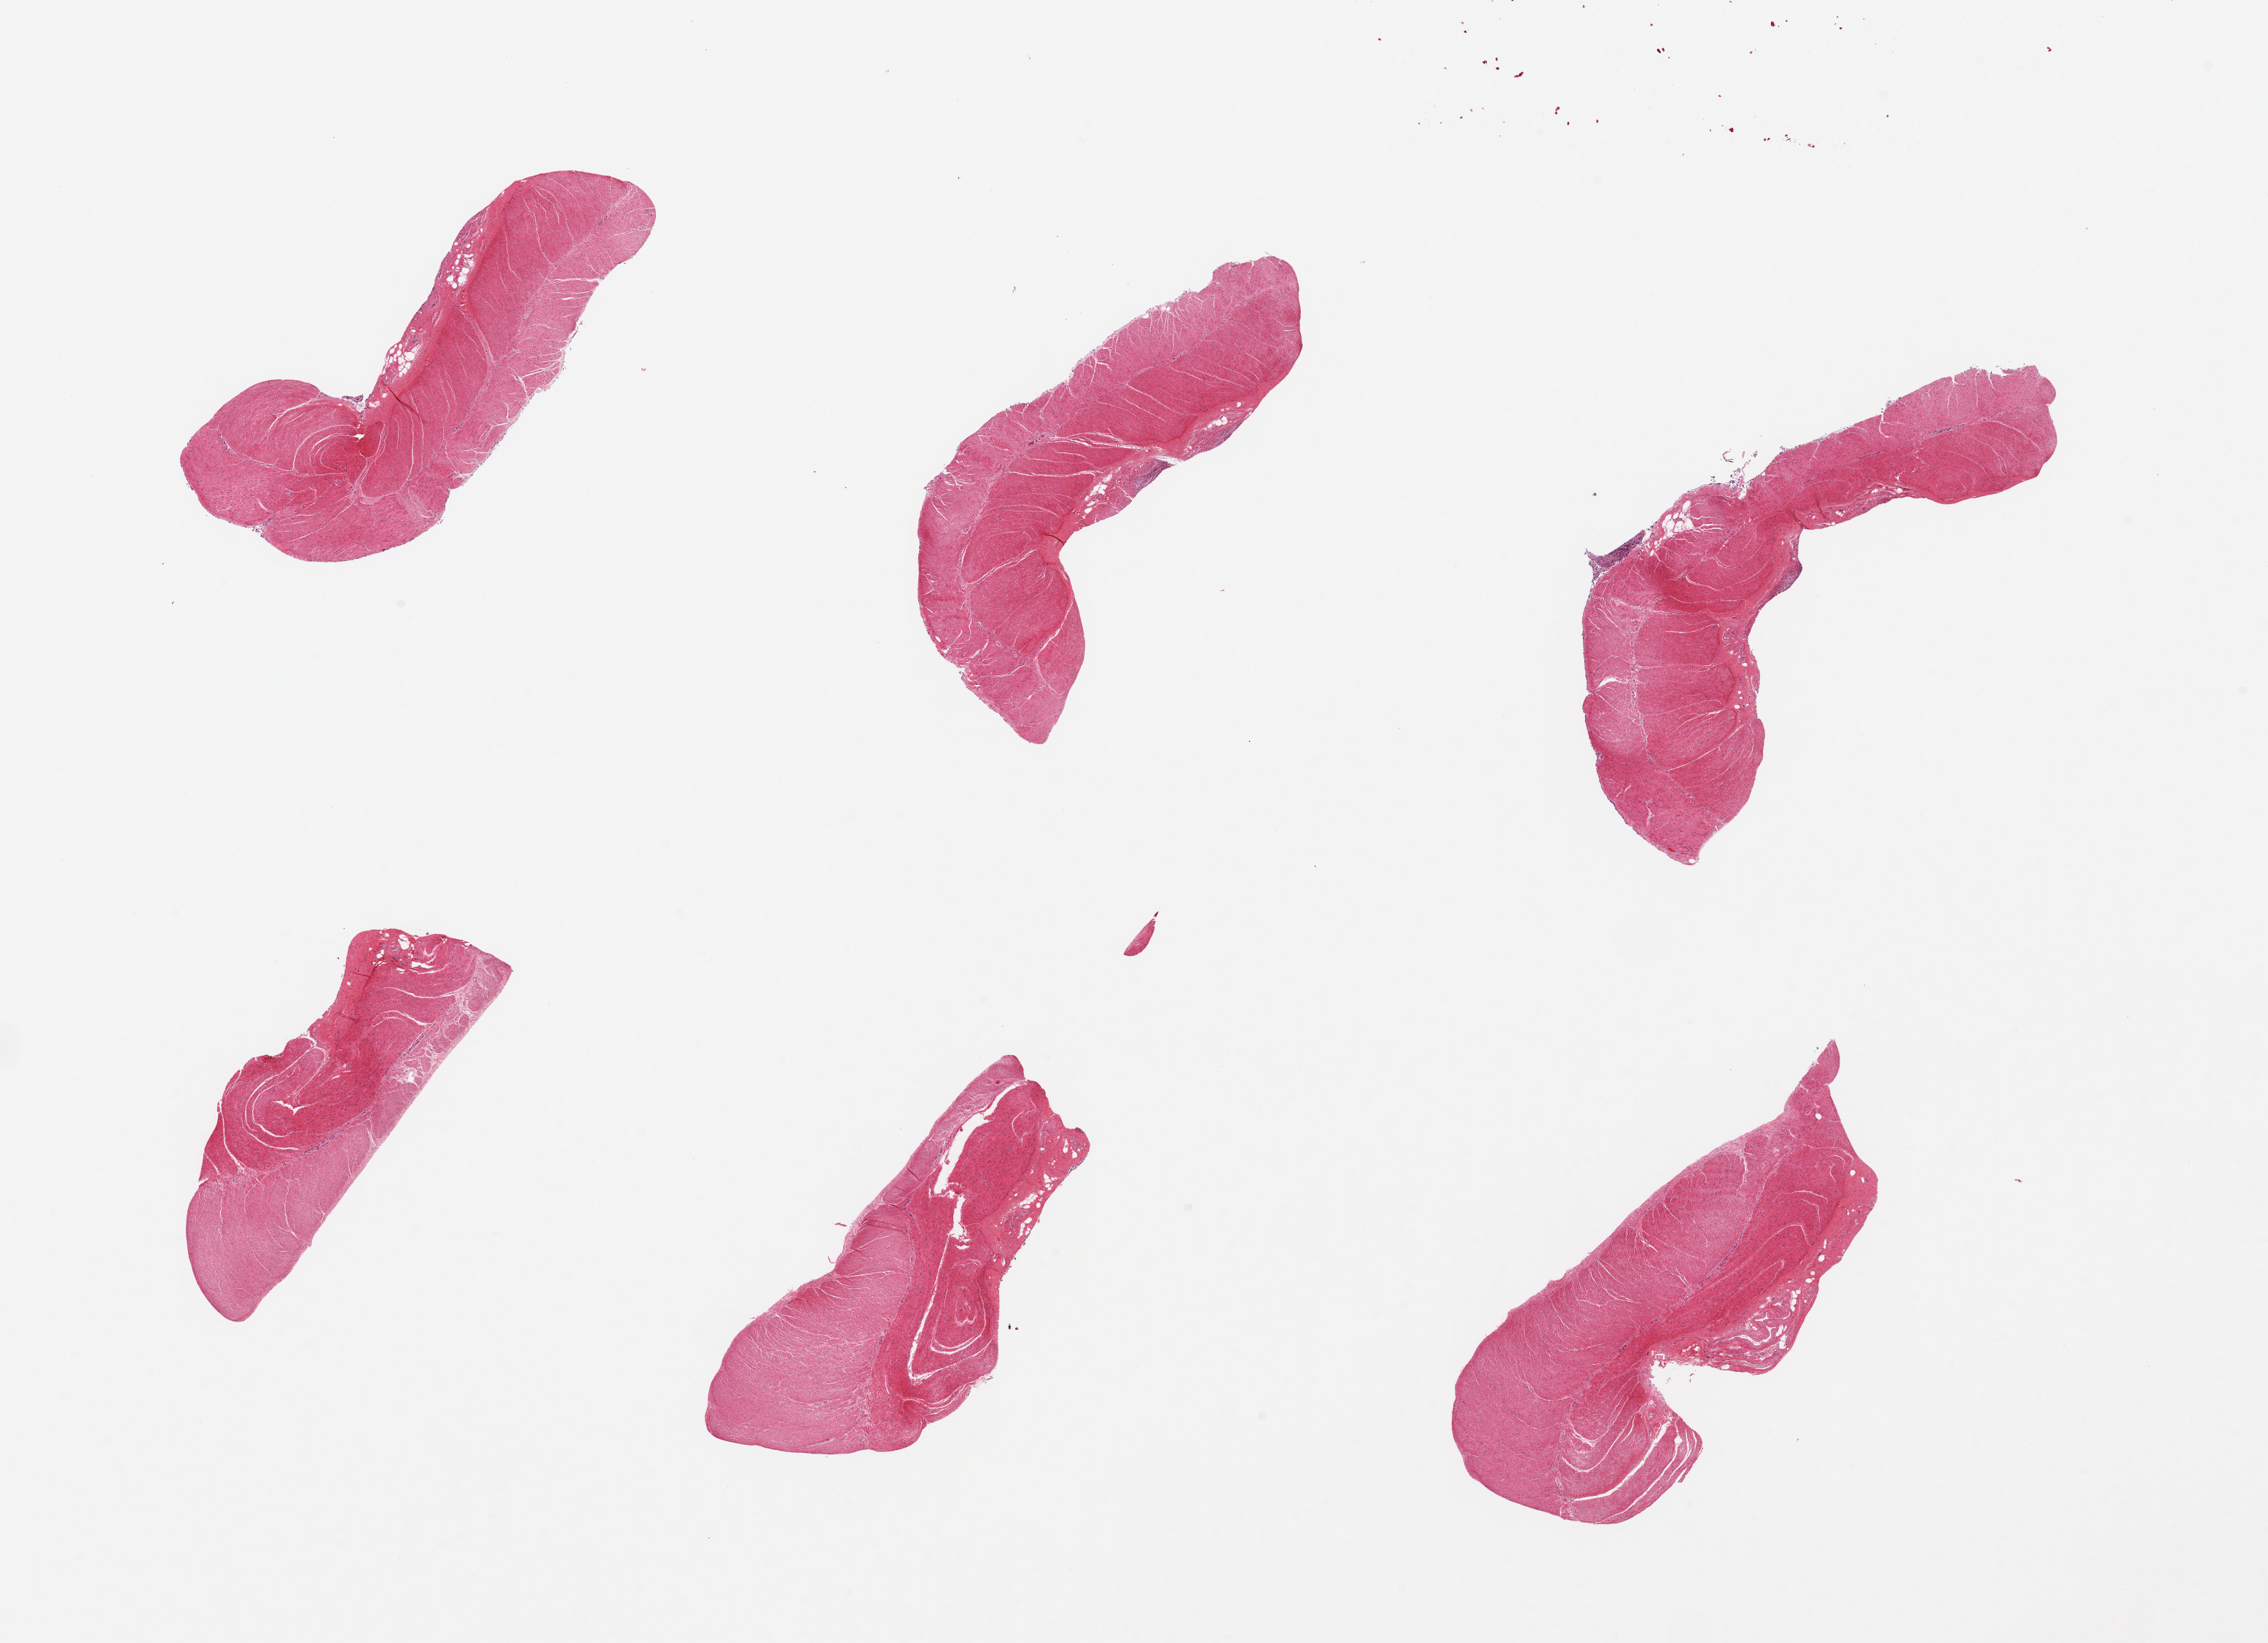
H&E whole-slide image — shown as a low-resolution overview of the whole scanned area (about 24.6 x 17.8 mm, acquisition: 20x scan); PAXgene-fixed, paraffin-embedded tissue; sampled site (target tissue): sigmoid colon; donor tissue sample. Donor: male.
Reviewer comment on this tissue sample: 6 pieces, confirmed target muscularis.